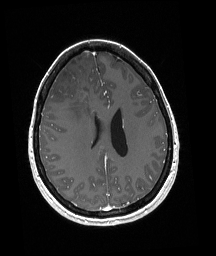
Brain MRI from a brain-tumour surgery series, one axial slice. Slice 76 of 192 in the series (ordered by position). T1-weighted post-contrast. 216 × 256 image matrix, field of view 211 × 250 mm. Case-level facts recorded for this patient, not image findings: histopathology: Oligodendroglioma; WHO grade: 3; IDH mutation: yes.
Outlined on this slice (expert manual segmentation):
- tumour: bounding box <60,82,86,91> (left, top, right, bottom; pixels)